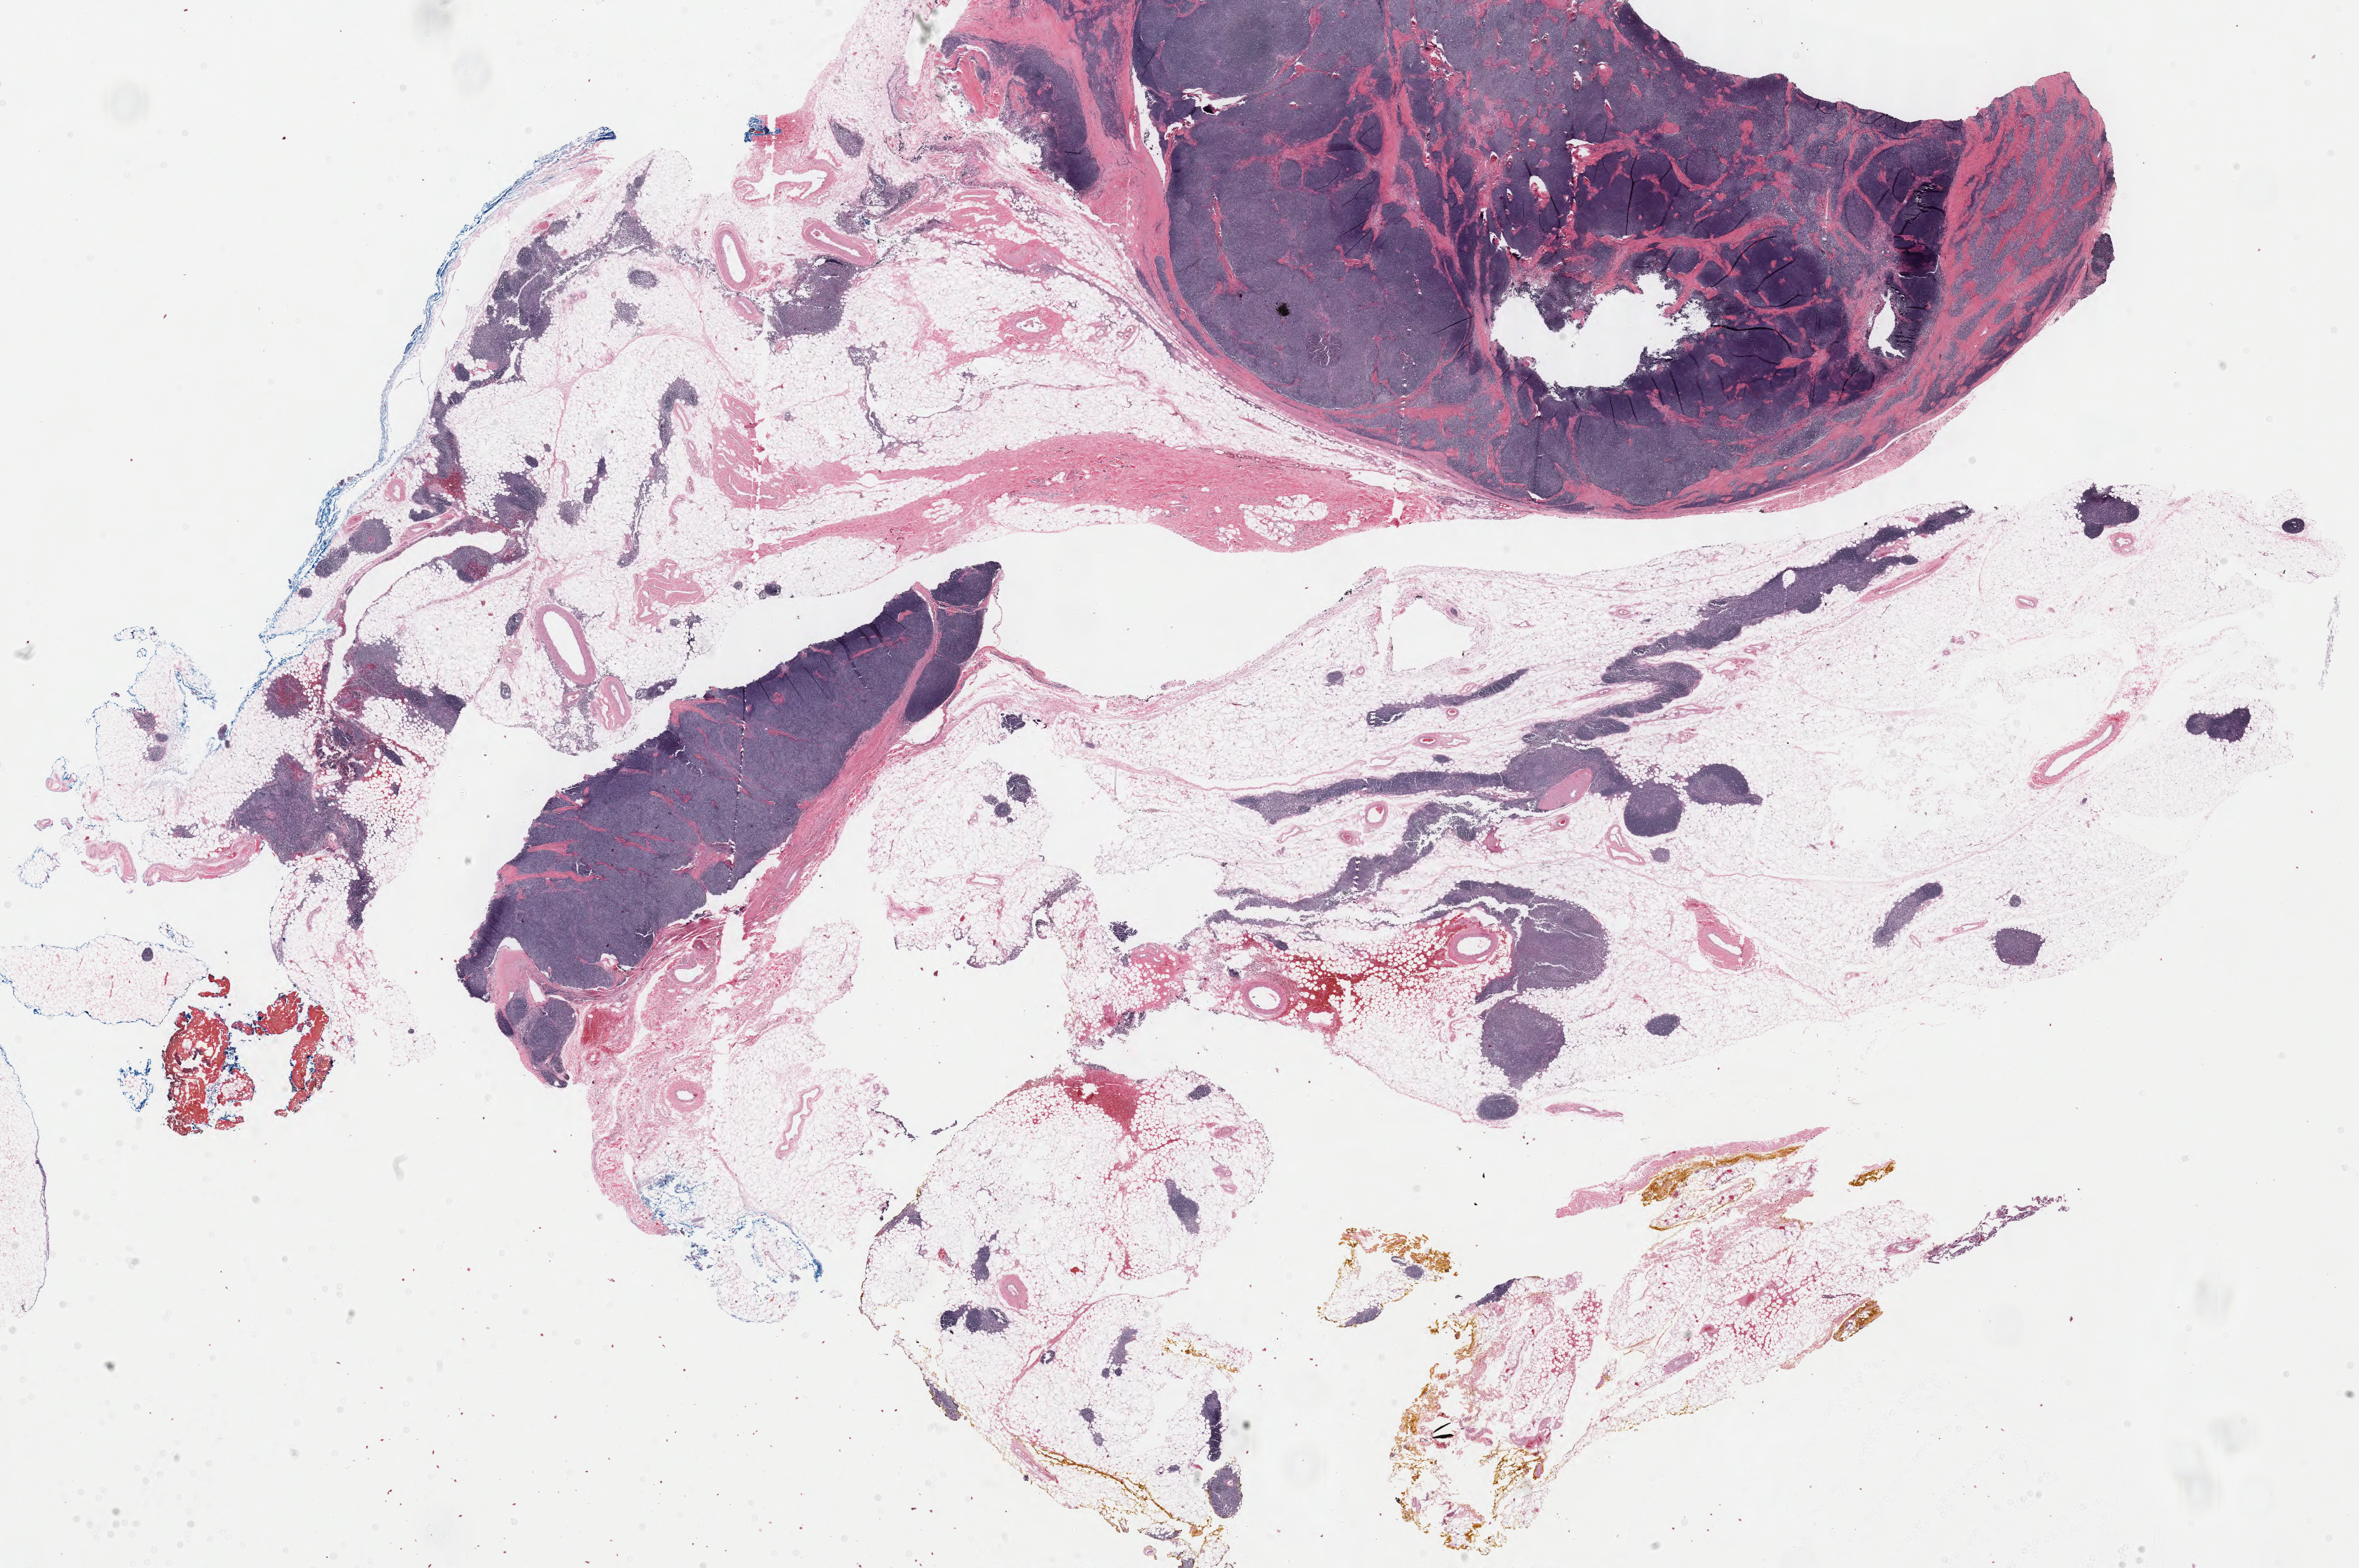
H&E whole-slide image, whole scanned area (about 29.4 x 19.6 mm, acquisition: 40x scan) shown as a low-resolution overview, formalin-fixed paraffin-embedded (FFPE) diagnostic section, primary tumour sample from the thymus. Female, age 50 years at initial diagnosis.
Diagnosis: Thymoma, type AB, malignant.